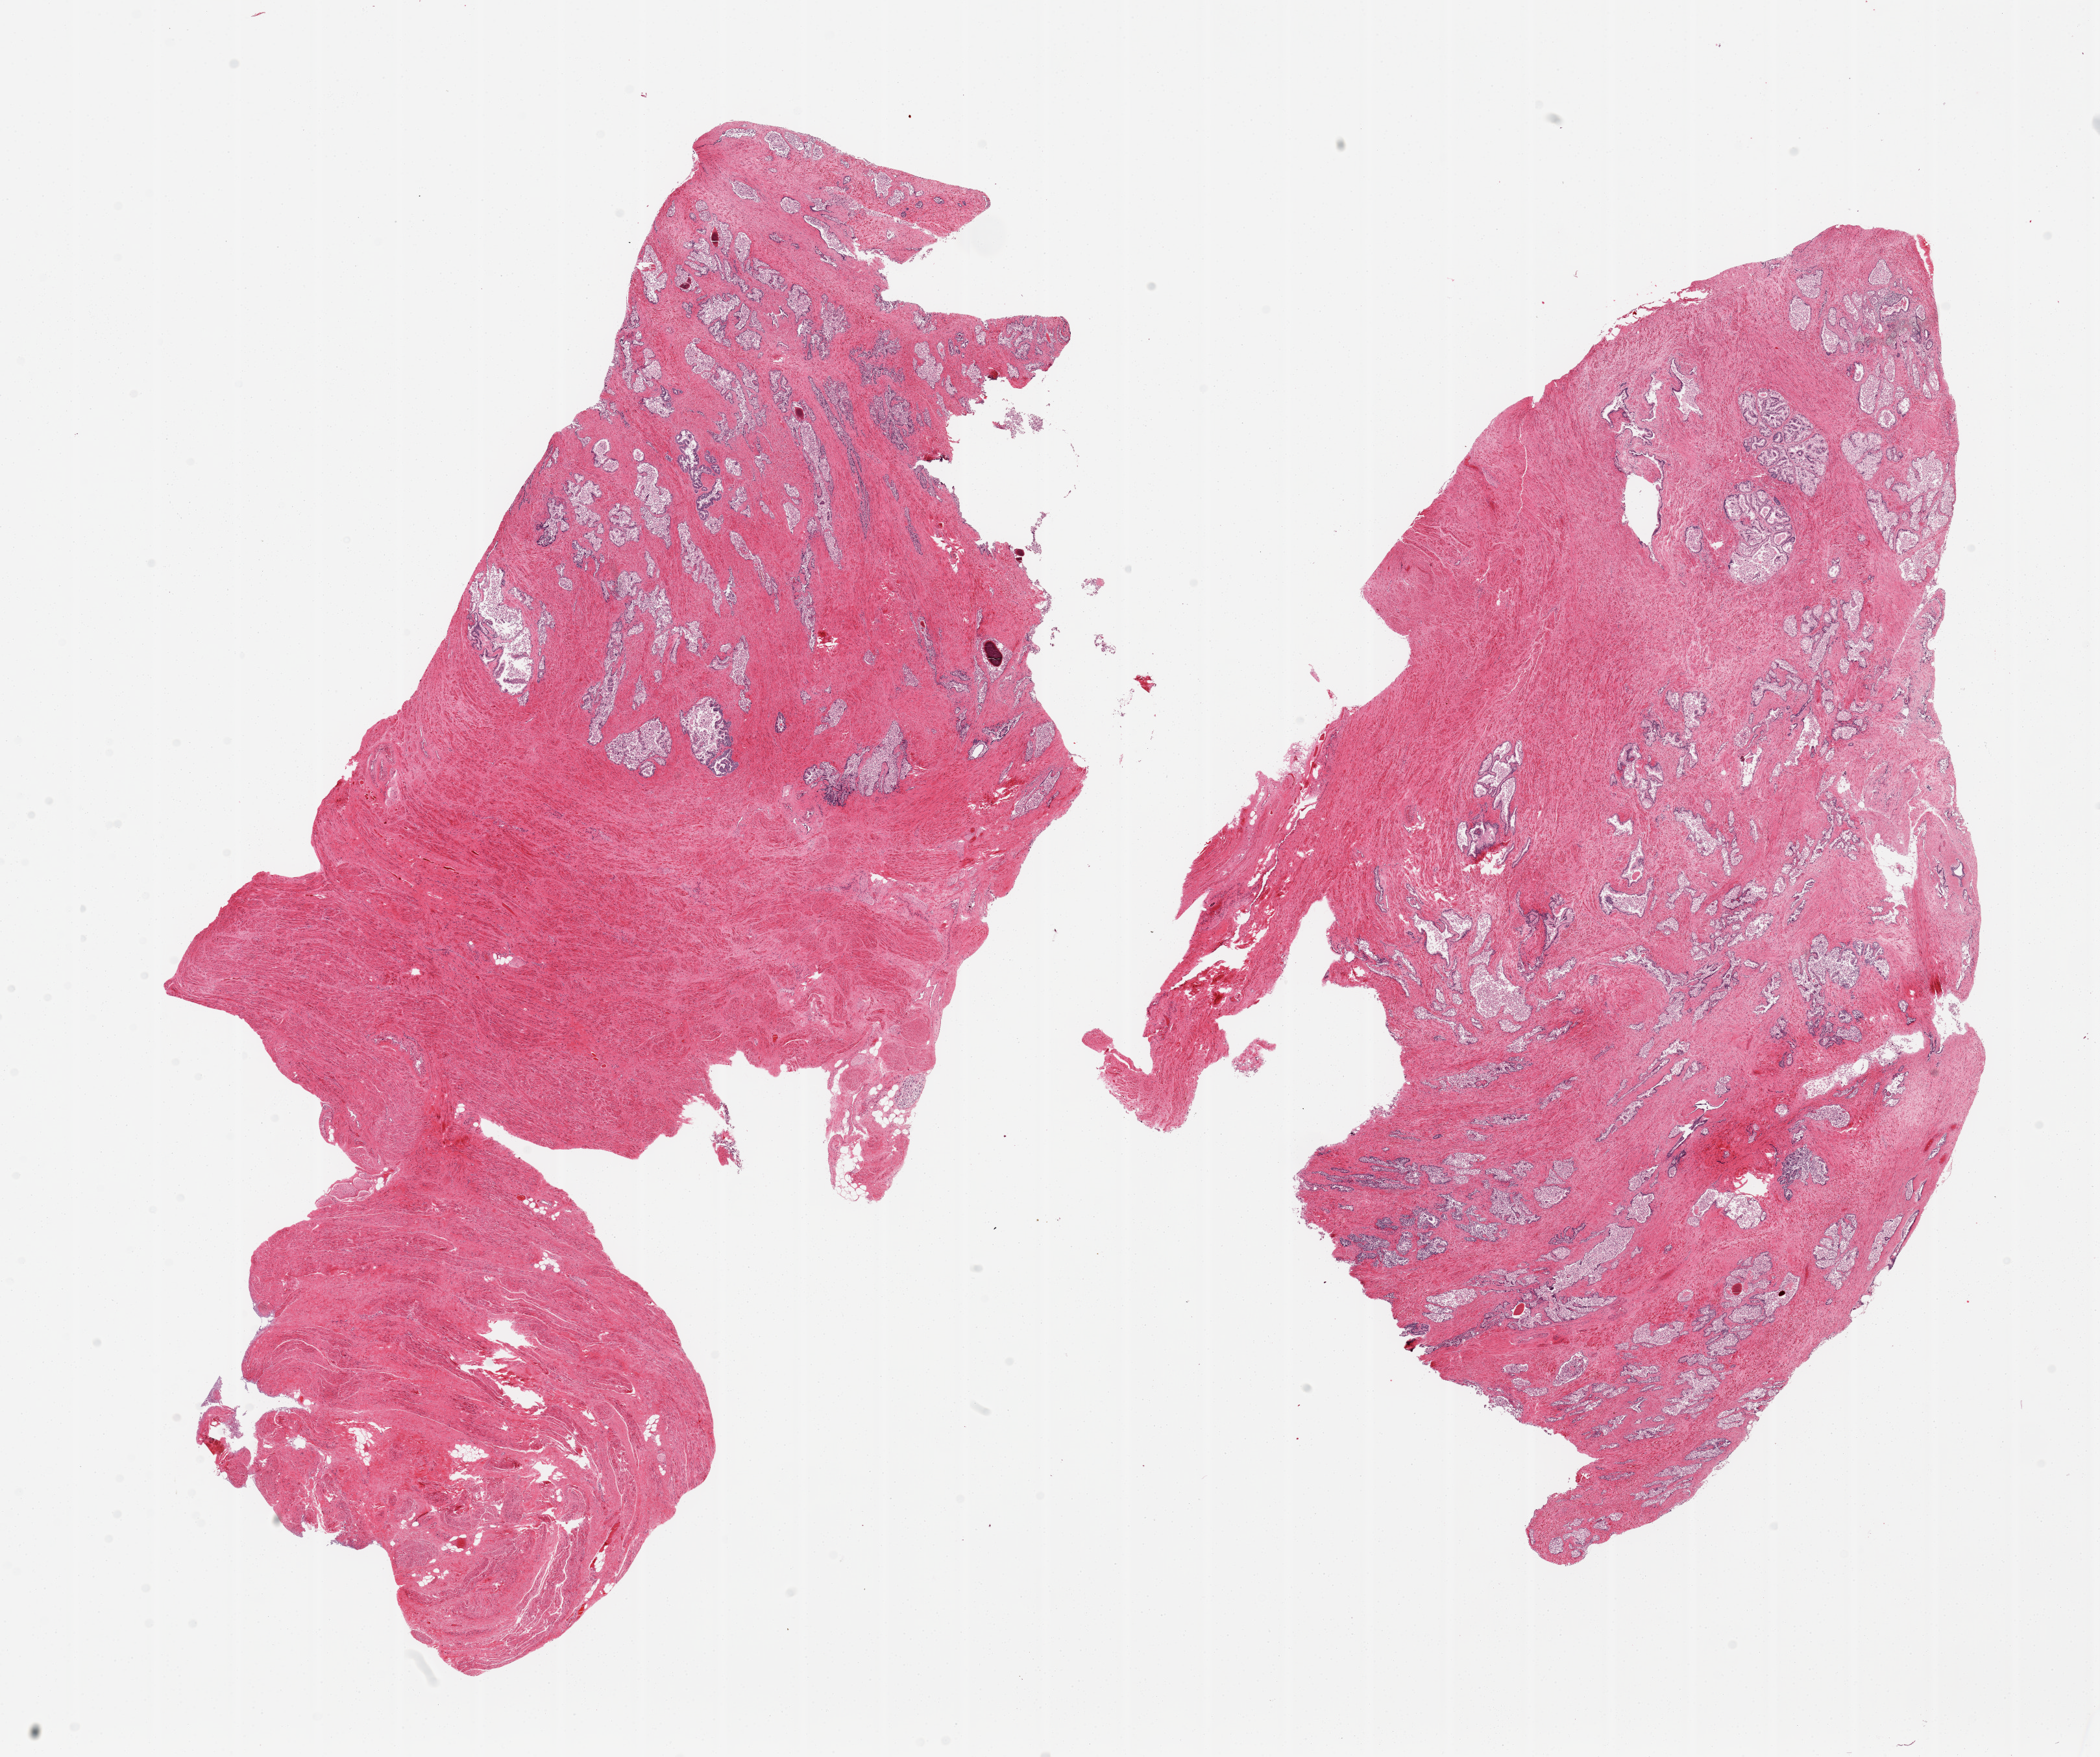
Digitized haematoxylin and eosin-stained section, brightfield — shown as a low-resolution overview of the whole scanned area (about 25.6 x 21.4 mm), PAXgene-fixed, paraffin-embedded tissue, sampled site (target tissue): prostate, tissue donor sample. Donor sex: male.
Pathologist's review note for this sample: 2 pieces; glands = 3; fibromuscular stroma = 1.